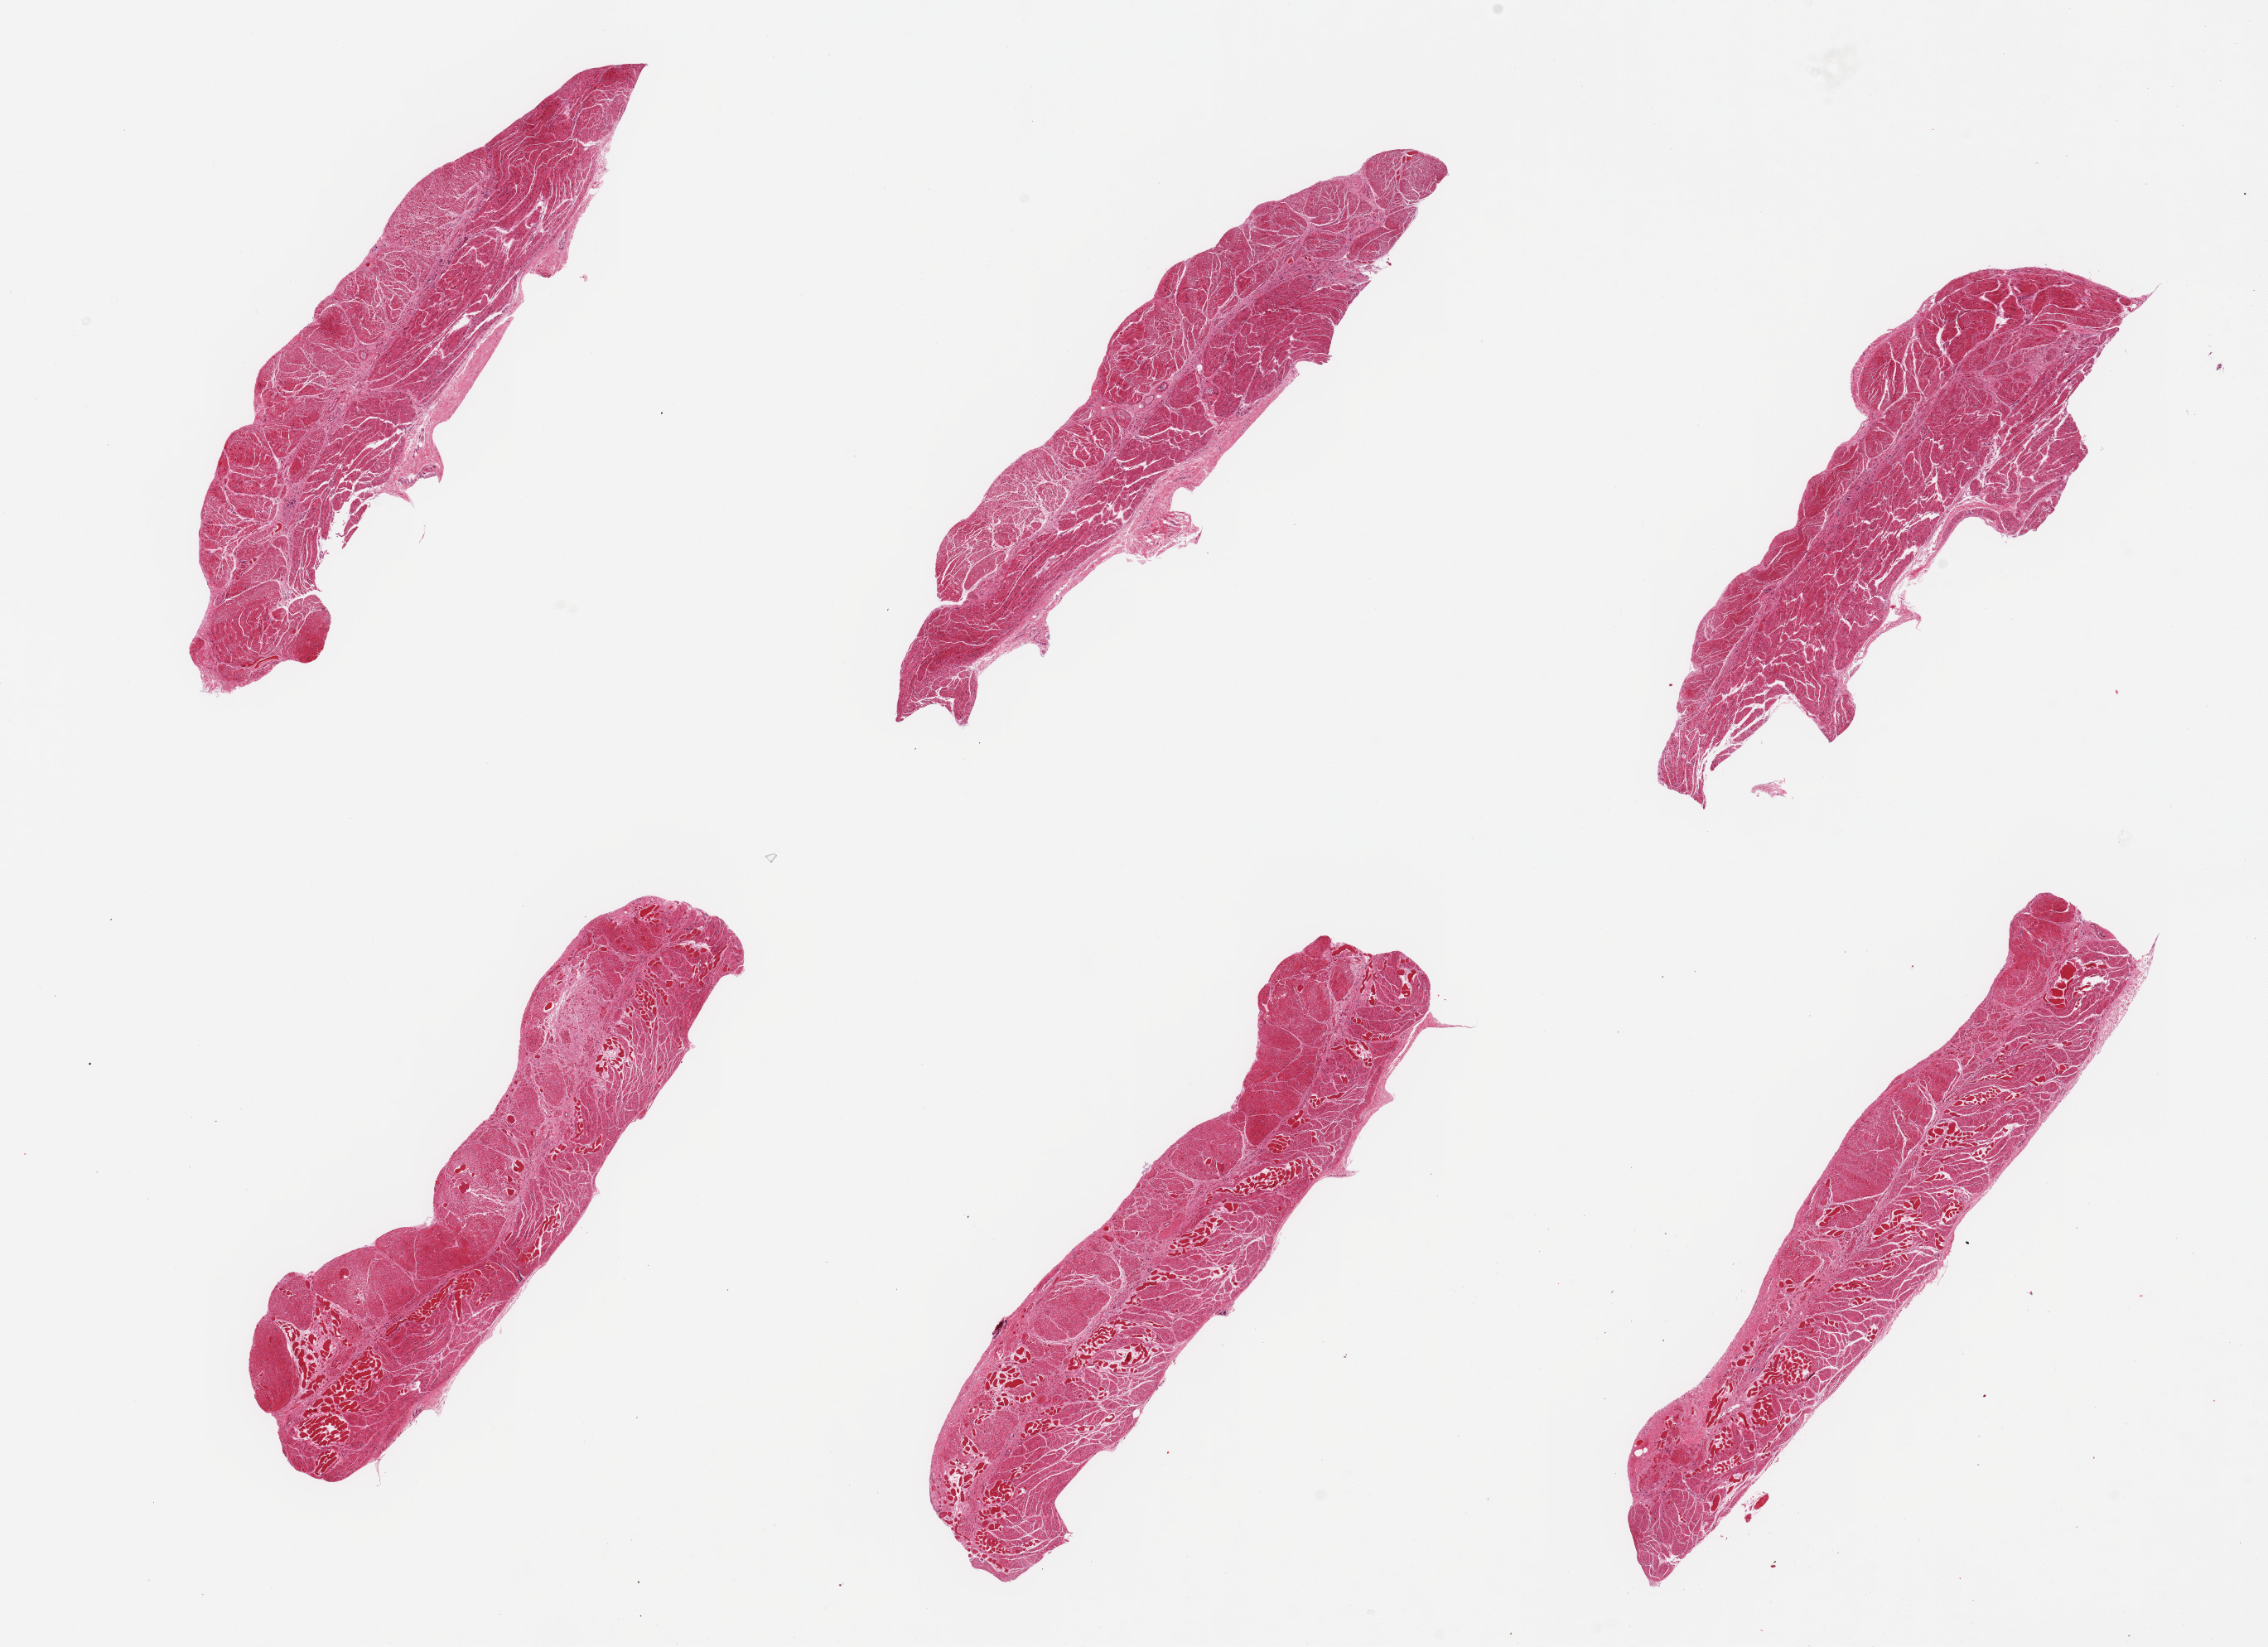
Whole-slide image, H&E stain, brightfield — a low-resolution overview of the entire scanned area, about 21.7 x 15.7 mm (from a 20x scan); PAXgene-fixed paraffin-embedded (PFPE) section; sampled site (target tissue): esophageal muscle; tissue donor sample.
• review note (as recorded): 6 pieces, confirmed target muscularis